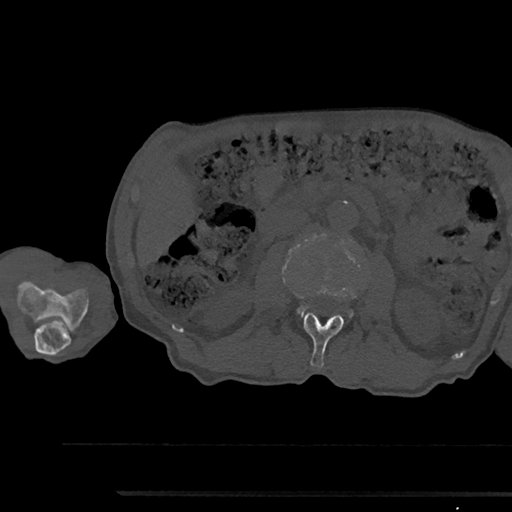
CT including the spine, one axial slice; position 535 of 797 along the scan axis; bone window (W 1800 / L 400 HU); 0.5 mm slice thickness; 512 × 512 image matrix, field of view 367 × 367 mm. Male patient, age 79 years. From the clinical record (not read from this slice): primary cancer: prostate.
Structures marked on this image (semi-automatically segmented with operator editing):
- L2 vertebra: bounding box <304,311,344,367> (left, top, right, bottom; pixels)
- L3 vertebra: <298,306,353,317>